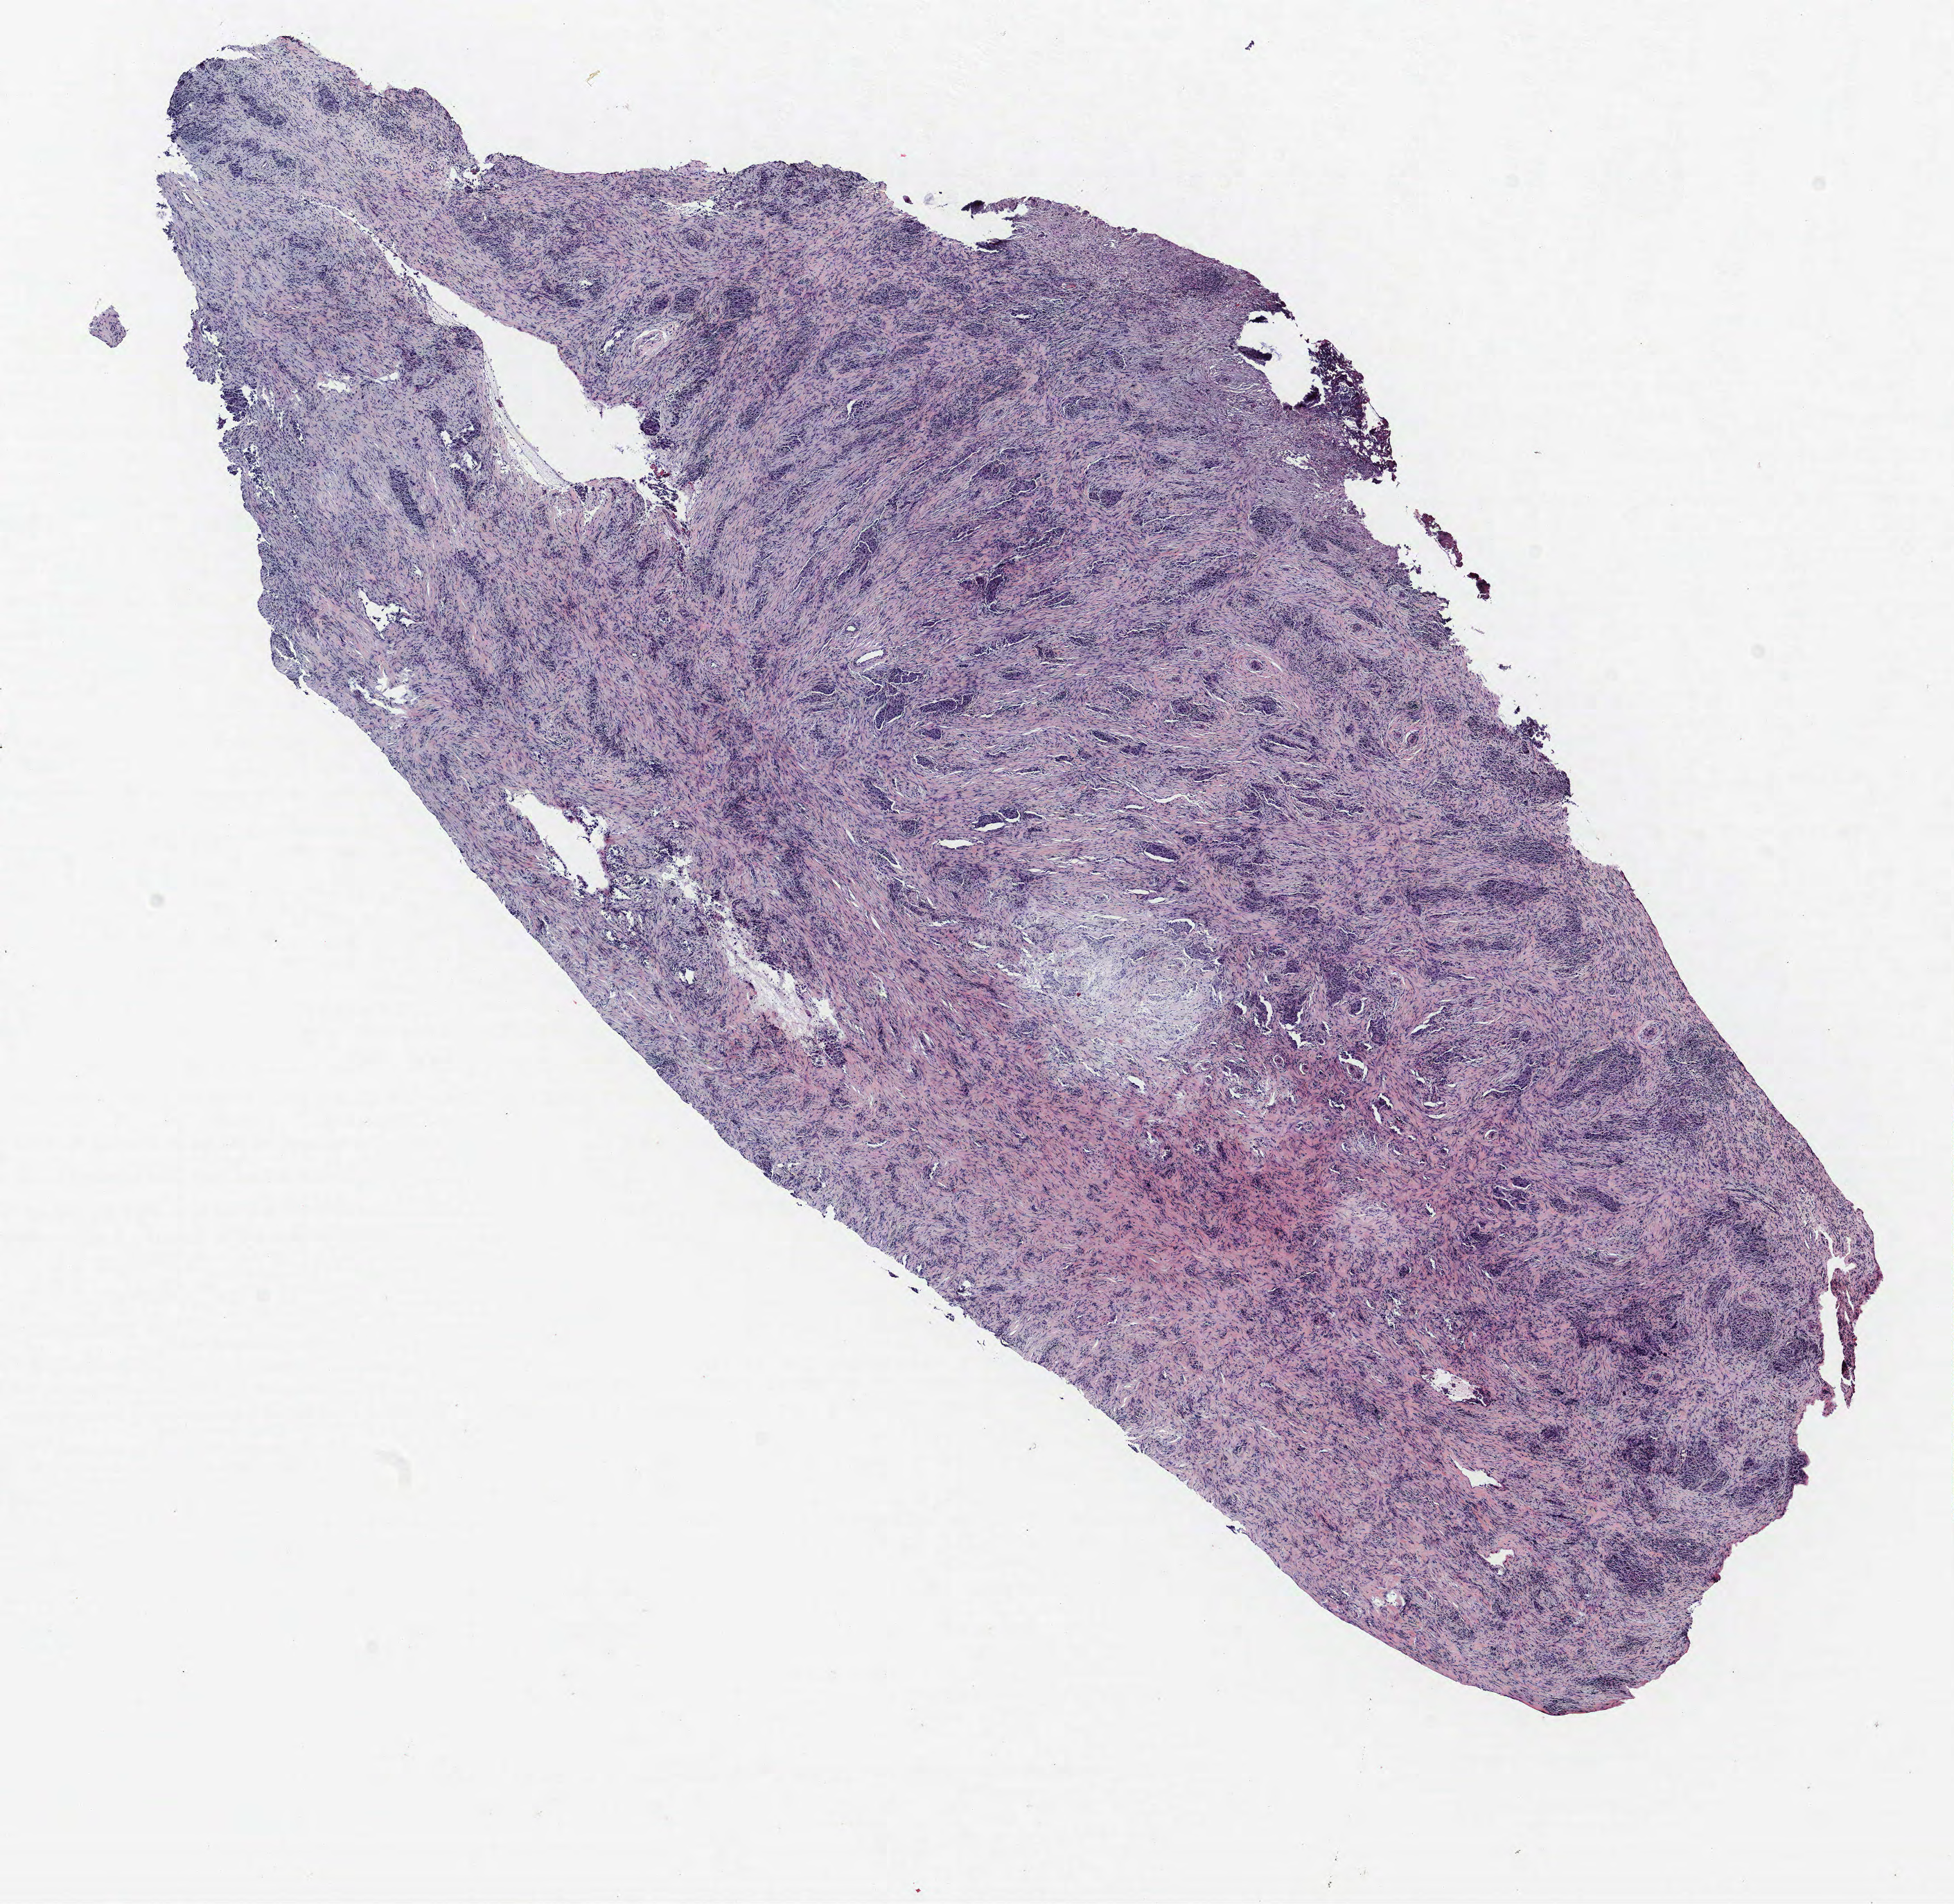
Whole-slide histology image, Hematoxylin and eosin (H&E) stained, whole scanned area (about 11.3 x 11.0 mm, acquisition: 40x scan) shown as a low-resolution overview; FFPE section; lung. Female, age 70 at enrolment. Former smoker at enrolment.
• stage (AJCC 6th edition): IV
• participant's lung-cancer diagnosis: Non-small cell carcinoma (ICD-O-3 8046/3)
• tumour size (pathology): 30 mm
• primary tumour location (clinical record): right upper lobe